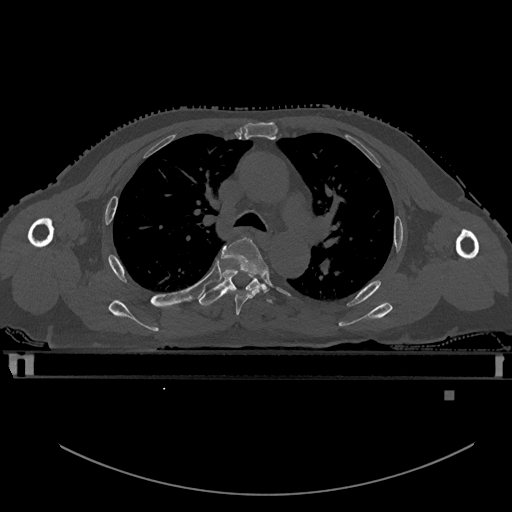
CT including the spine, one axial slice; slice 383 of 969 in the series (ordered by position); bone window (W 1800 / L 400 HU); 512 × 512 image matrix, field of view 456 × 456 mm. Patient: male, 82 years. Case-level facts recorded for this patient, not image findings: primary cancer: prostate.
Outlined on this slice (semi-automatically segmented with operator editing):
- T4 vertebra: bounding box (x1, y1, x2, y2) in pixels: (221, 237, 268, 315)
- T5 vertebra: (199, 270, 273, 306)